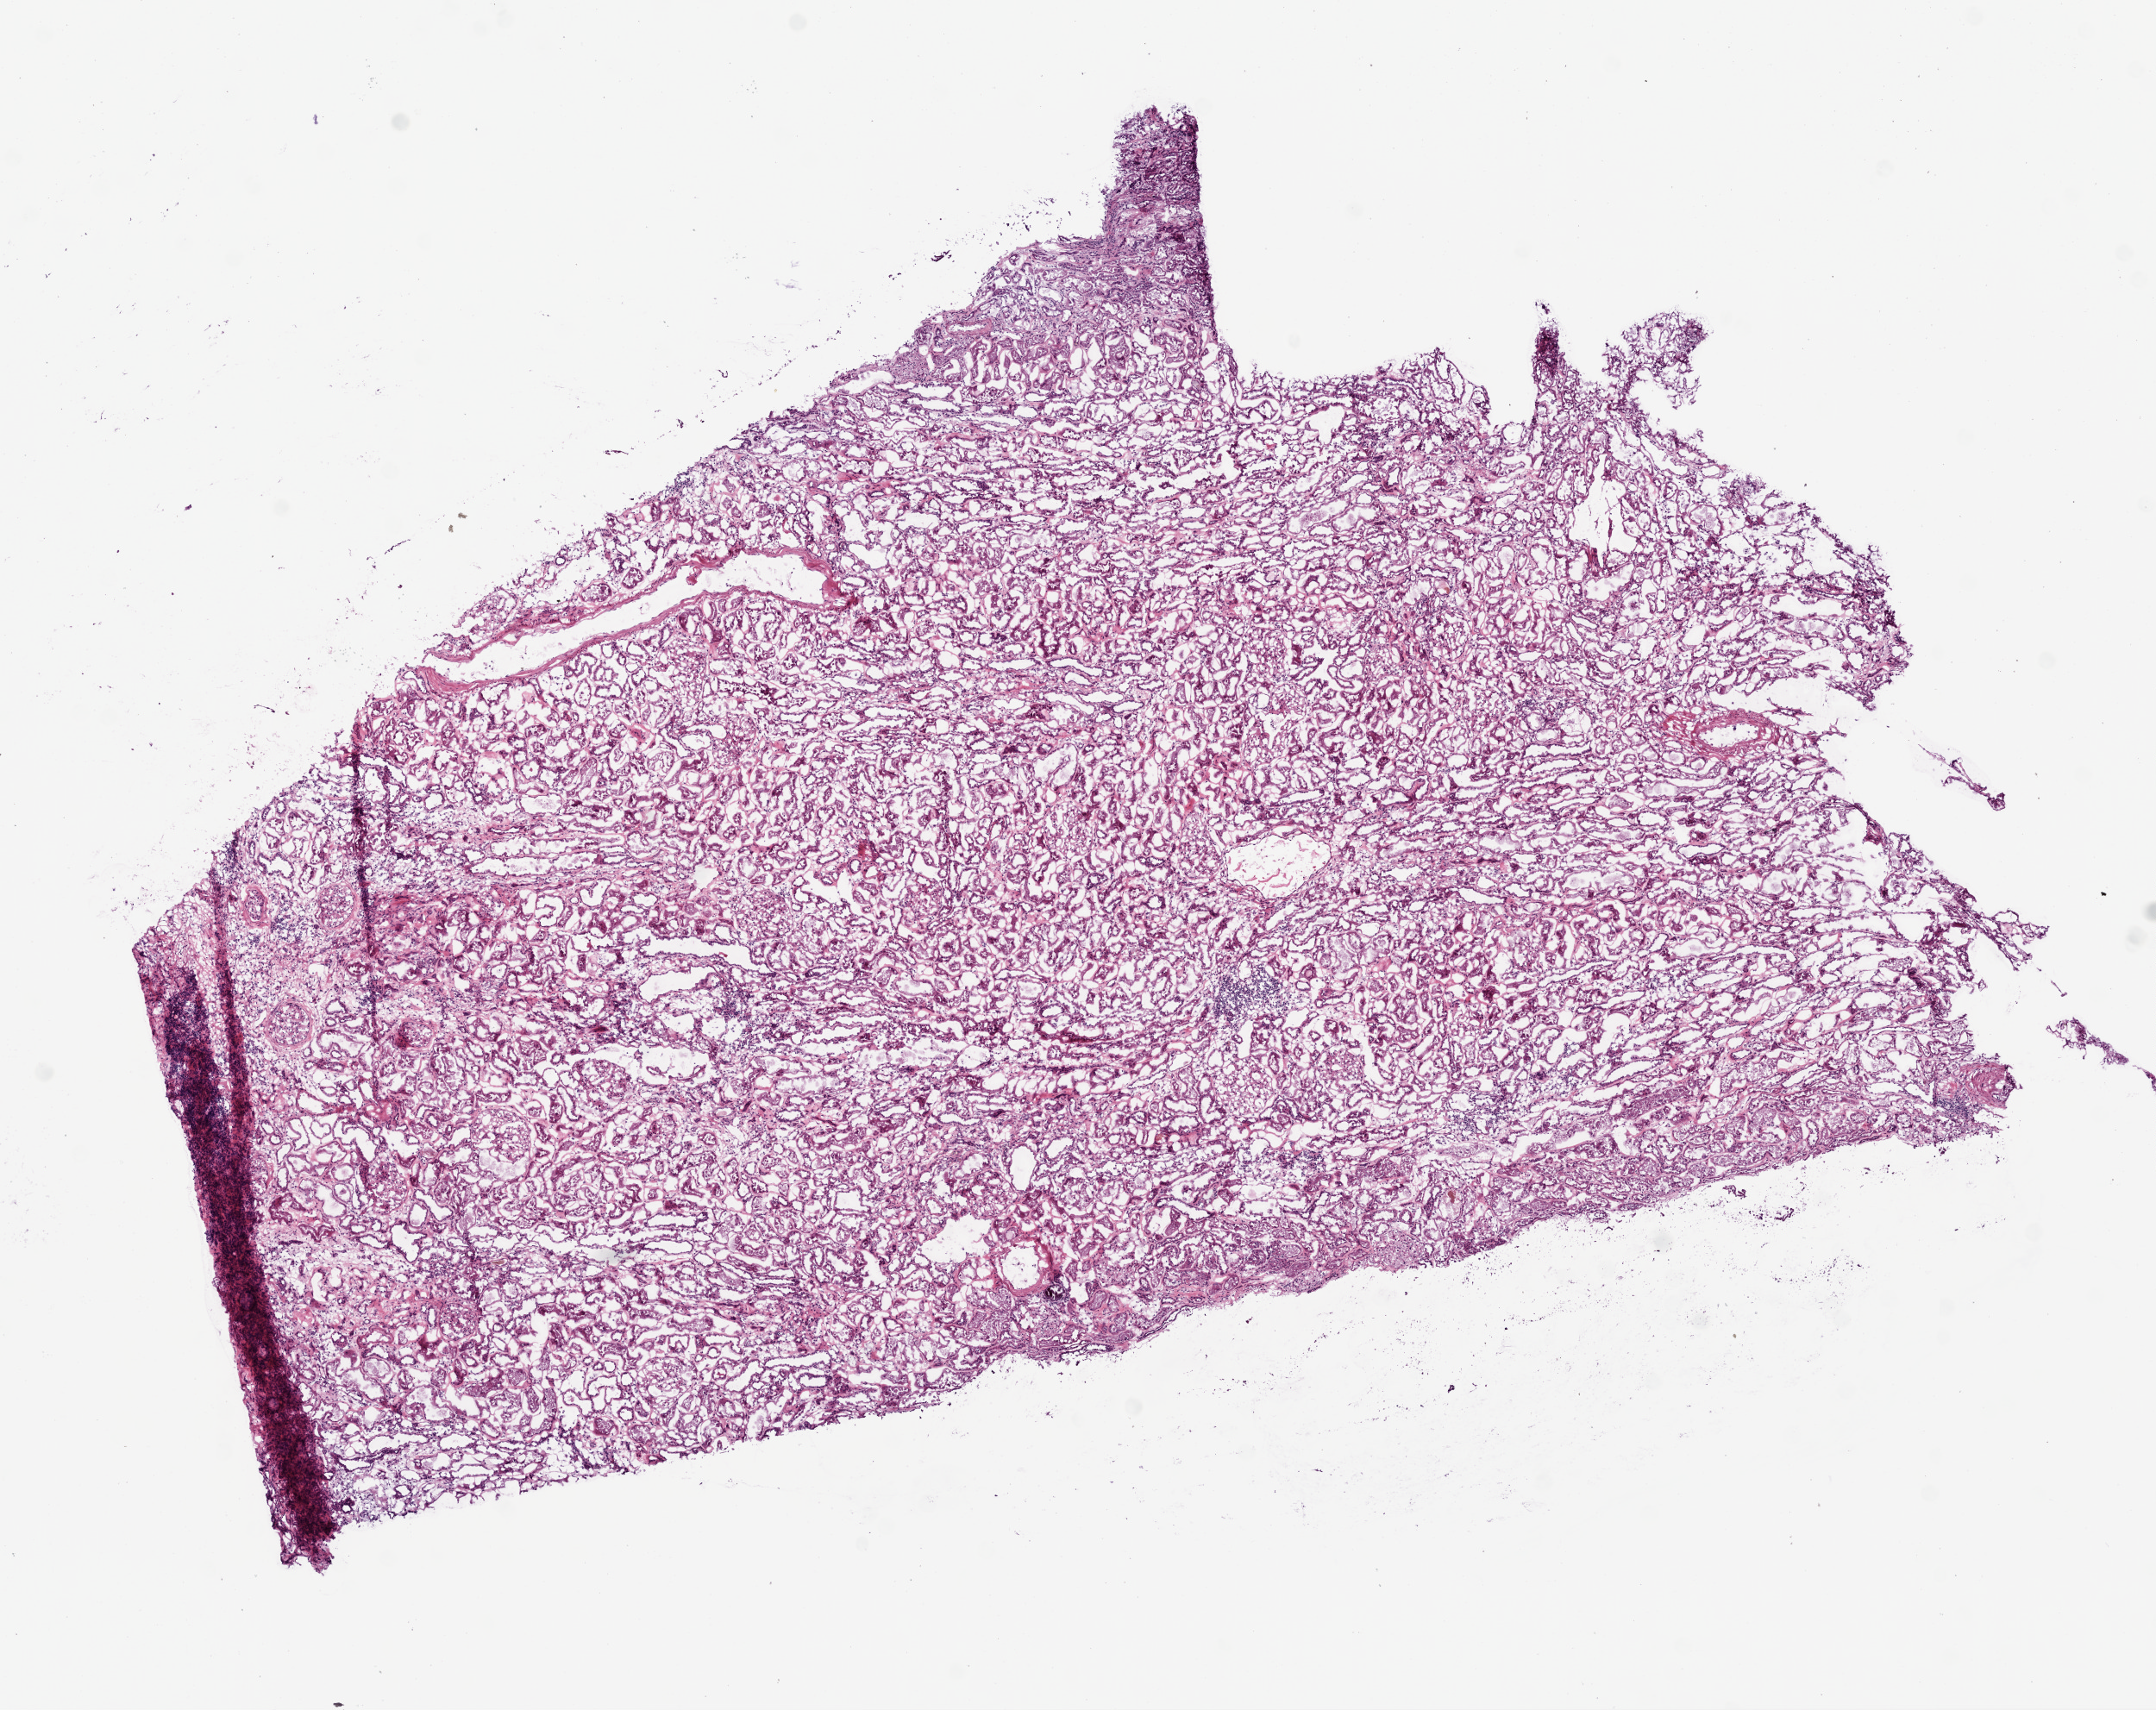
Digitized H&E tissue section (whole slide), low-resolution overview of the scanned area, about 10.0 x 8.0 mm (slide scanned at 20x). Frozen section from the bottom of the tissue portion. Sample: solid tissue normal (non-tumour tissue), kidney. Male patient; age at initial diagnosis 63 years.
* this section: solid tissue normal sample (biorepository sample class)
* patient diagnosis: Clear cell adenocarcinoma, NOS